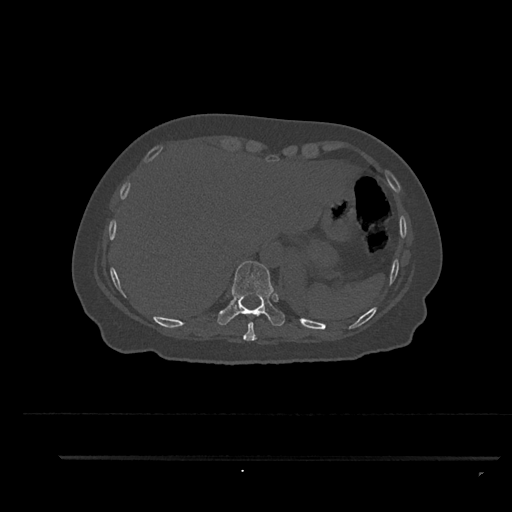
CT including the spine, one axial slice; slice 374 of 797 in the series (ordered by position); bone window (W 1800 / L 400 HU); 0.5 mm slice thickness; 512 × 512 image matrix, field of view 408 × 408 mm. Female patient, age 44 years. From the clinical record (not read from this slice): primary cancer: renal; vertebrae with lytic lesions (as recorded): L1.
Annotated regions visible in this slice (semi-automatically segmented with operator editing):
- T10 vertebra: bounding box <217,260,285,326> (left, top, right, bottom; pixels)
- T9 vertebra: <243,322,257,341>